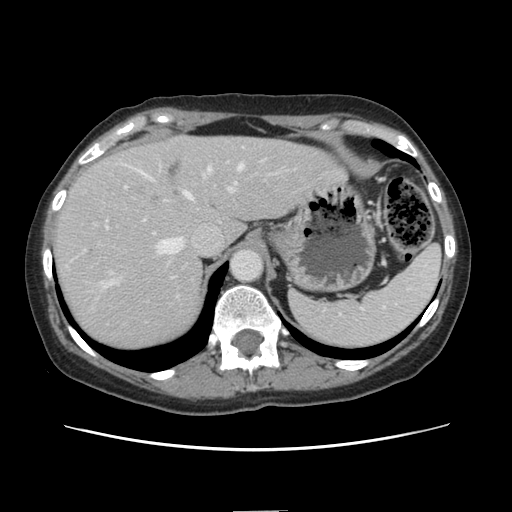
Contrast-enhanced abdominal CT, one axial slice. Position 108 of 141 along the scan axis. 120 kVp. Intravenous contrast given. Soft-tissue window (W 400 / L 40 HU). 512 × 512 image matrix, field of view 350 × 350 mm. Female patient, age 63 years. Case-level facts recorded for this patient, not image findings: diagnosis: colorectal cancer liver metastases, imaged before liver resection; multiple liver metastases: yes; largest metastasis: 3.2 cm; disease in both lobes: yes.
Outlined on this slice (outlined manually by an expert reader):
- hepatic veins: bounding box (x1, y1, x2, y2) in pixels: (100, 164, 243, 289)
- liver: (53, 136, 342, 351)
- planned liver remnant (the part of the liver to remain after resection): (188, 137, 344, 242)
- portal vein (with intrahepatic branches): (203, 171, 236, 192)